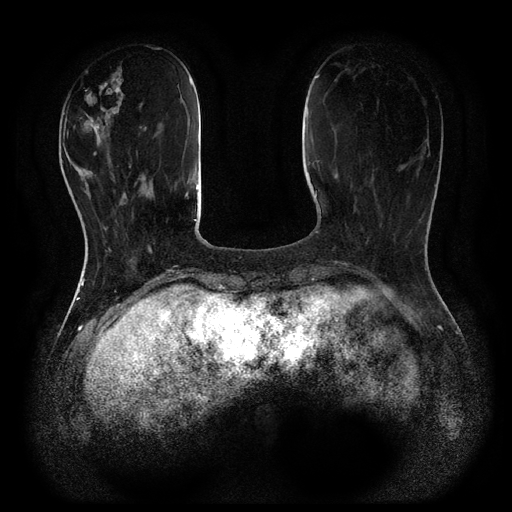
Breast MRI (dynamic contrast-enhanced, multi-phase), one axial slice. Slice 28 of 116 in the series (ordered by position). Dynamic contrast-enhanced series, time point 2 of 5 at this slice position (early post-contrast). 1.5 T. TE 2.6 ms, TR 5.4 ms. 512 × 512 image matrix, field of view 340 × 340 mm. Patient: female, 48 years.
Structures marked on this image (semi-automatic segmentation, software-assisted and operator-edited):
- breast lesion (labelled benign in the annotation): bounding box (x1, y1, x2, y2) in pixels: (76, 66, 125, 147)